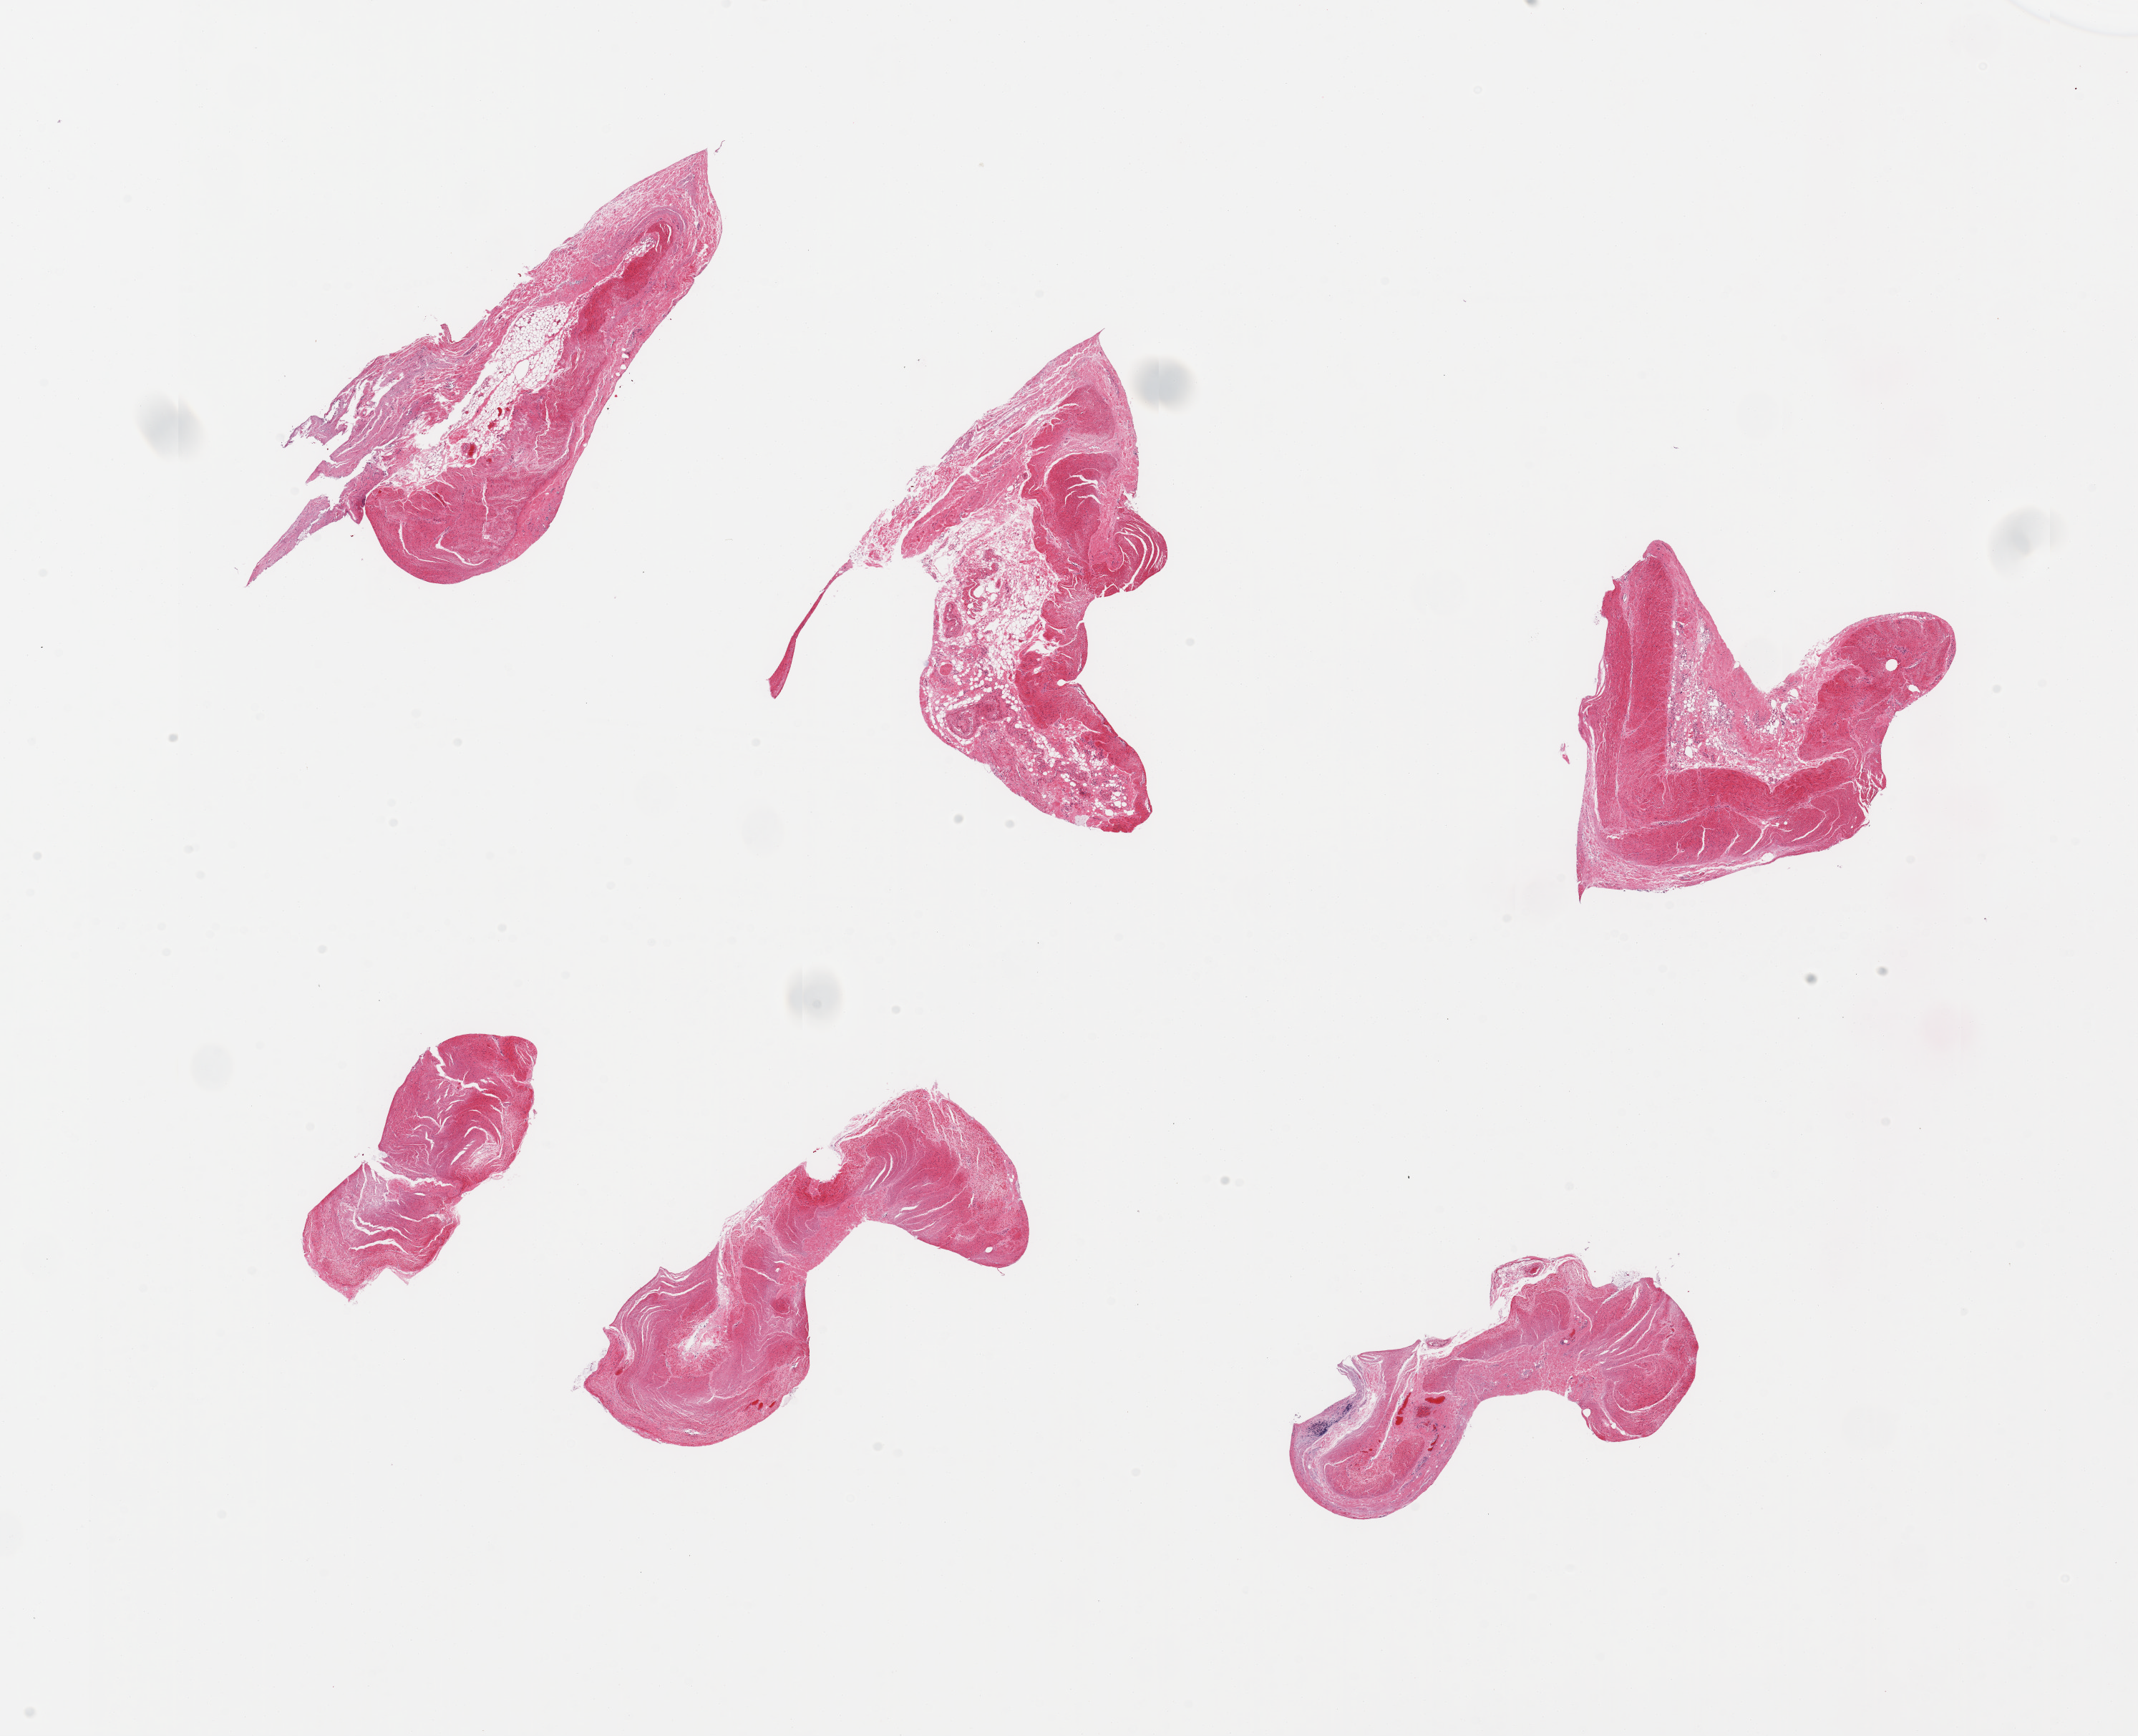
Digitized H&E-stained section, low-resolution overview of the scanned area, about 23.6 x 19.2 mm. PAXgene-fixed, paraffin-embedded tissue. Sampled site (target tissue): sigmoid colon. Donor tissue sample.
Review note (as recorded): 6 pieces; target muscularis, but up to 50% attached fat, submucosa.